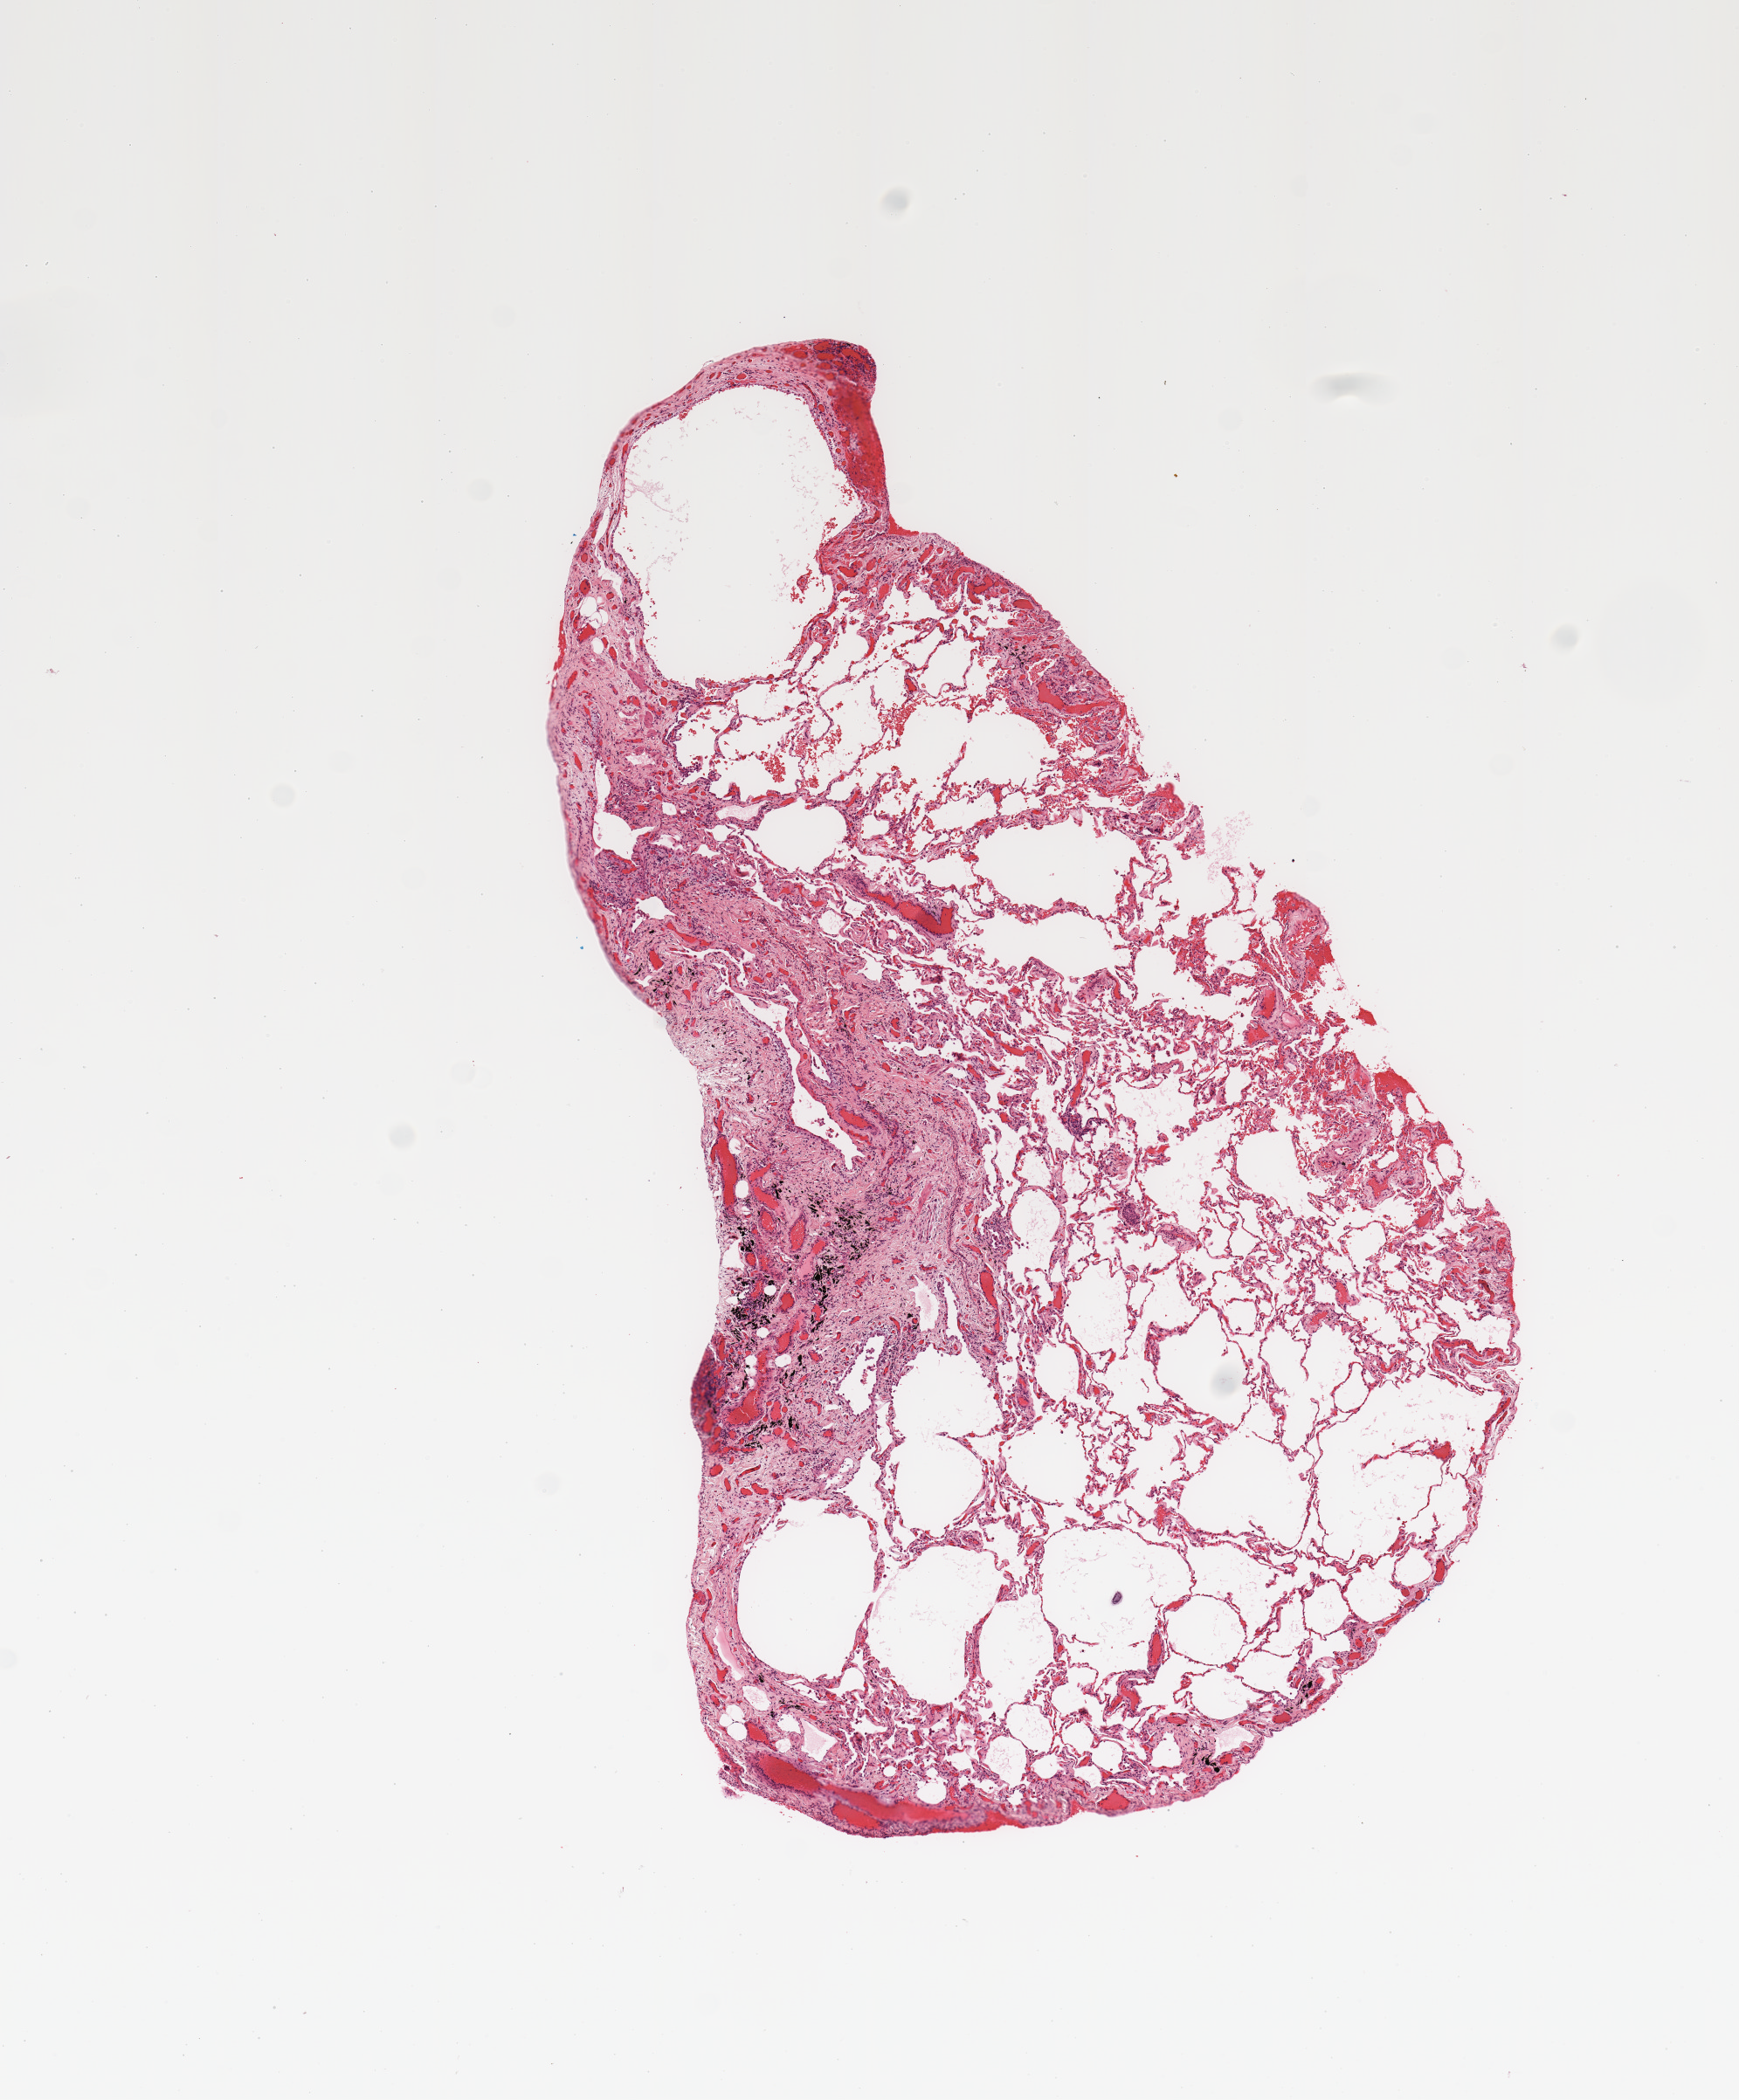
Whole-slide histology image, H&E-stained, shown as a low-resolution overview of the whole scanned area (about 7.9 x 9.5 mm, from a 20x scan); normal (non-tumour) tissue sample, sampled site: lung. 70-year-old male patient.
* this section: normal (non-tumour) tissue from the same patient
* patient diagnosis: Squamous cell carcinoma, NOS